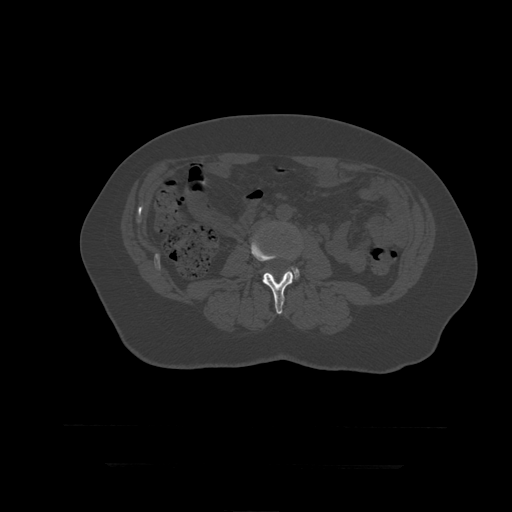
CT including the spine, one axial slice; slice 115 of 399 in the series (ordered by position); reconstruction kernel STANDARD; bone window (W 1800 / L 400 HU); 512 × 512 image matrix, field of view 450 × 450 mm. Patient age 41 years. Case-level facts recorded for this patient, not image findings: primary cancer: breast.
Outlined on this slice (semi-automatic segmentation, software-assisted and operator-edited):
- L3 vertebra: box from (x=251, y=235) to (x=294, y=314) px
- L4 vertebra: (x=290, y=257)–(x=300, y=280)